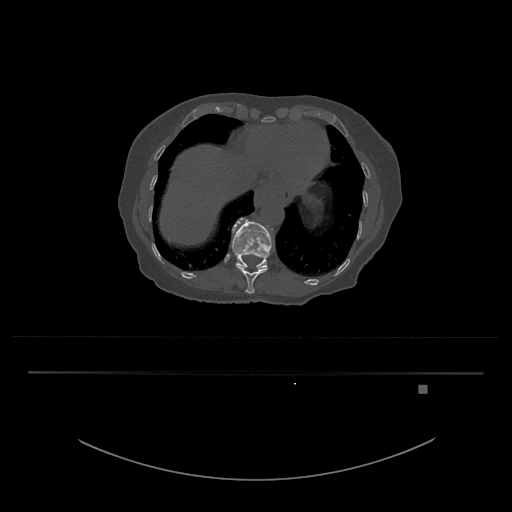
CT including the spine, one axial slice. Position 641 of 797 along the scan axis. Bone window (W 1800 / L 400 HU). 0.5 mm slice thickness. 512 × 512 image matrix, field of view 500 × 500 mm. Patient: female, 57 years. Case-level facts recorded for this patient, not image findings: primary cancer: cervical.
Outlined on this slice (semi-automatically segmented with operator editing):
- T11 vertebra: bounding box (x1, y1, x2, y2) in pixels: (236, 265, 268, 294)
- T12 vertebra: (232, 218, 271, 269)